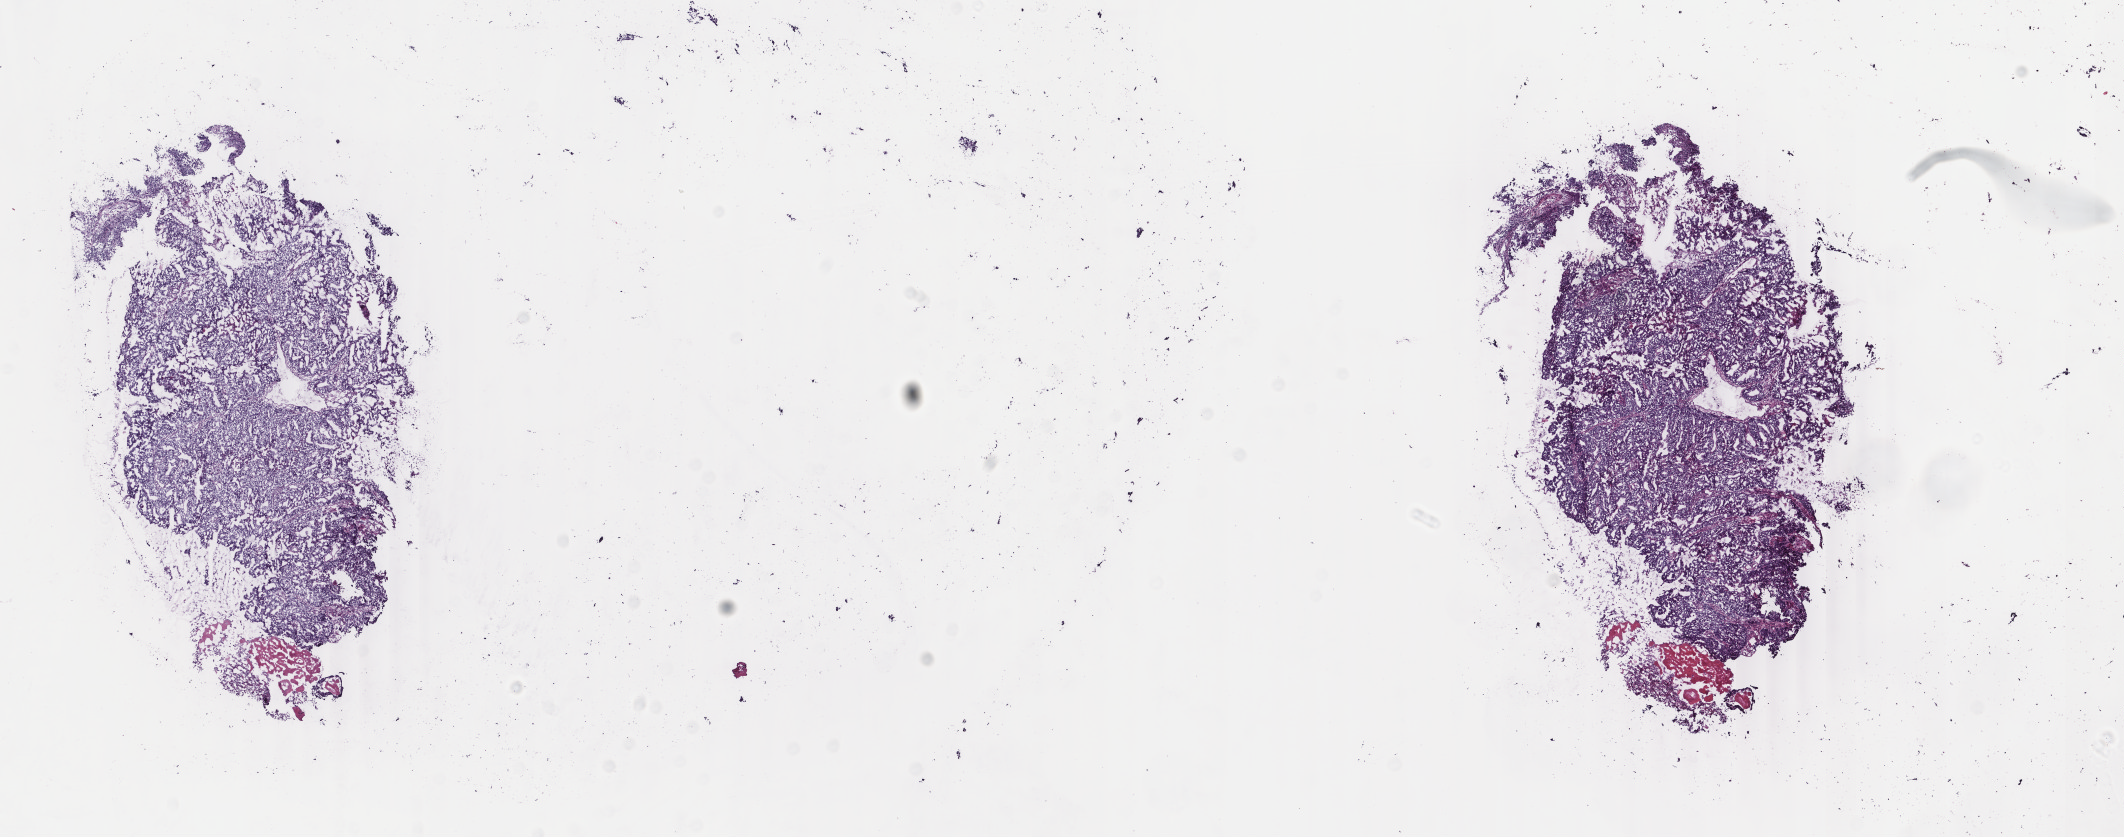
Digitized H&E-stained tissue section (whole slide) — low-resolution overview of the scanned area, about 16.9 x 6.7 mm (slide scanned at 40x), frozen section from the top of the tissue portion, sample: primary tumour, uterus. Female, age 58 years at initial diagnosis. Histologic grade: G3 (poorly differentiated). Pathologist review of this section (percent, as recorded): tumour cells 80%, tumour nuclei 80%, normal cells 0%, stromal cells 15%, necrosis 5%. Infiltration values recorded for this section: lymphocyte infiltration 40%, monocyte infiltration 20%, neutrophil infiltration 20%.
- FIGO stage: IB
- histologic diagnosis: Endometrioid adenocarcinoma, NOS (endometrium)